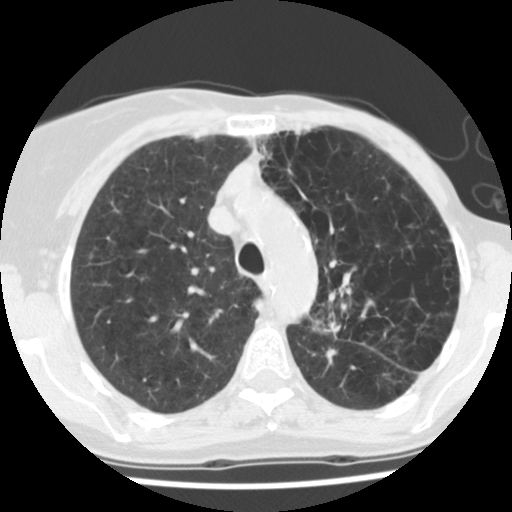
Low-dose screening chest CT, one axial slice; slice 94 of 128 in the series (ordered by position); lung window (W 1500 / L -600 HU); 512 × 512 image matrix.
Annotated regions visible in this slice (expert manual segmentation):
- lesion 1 (tumor, upper lobe of left lung): bounding box [x1, y1, x2, y2] px = [313, 312, 341, 333]